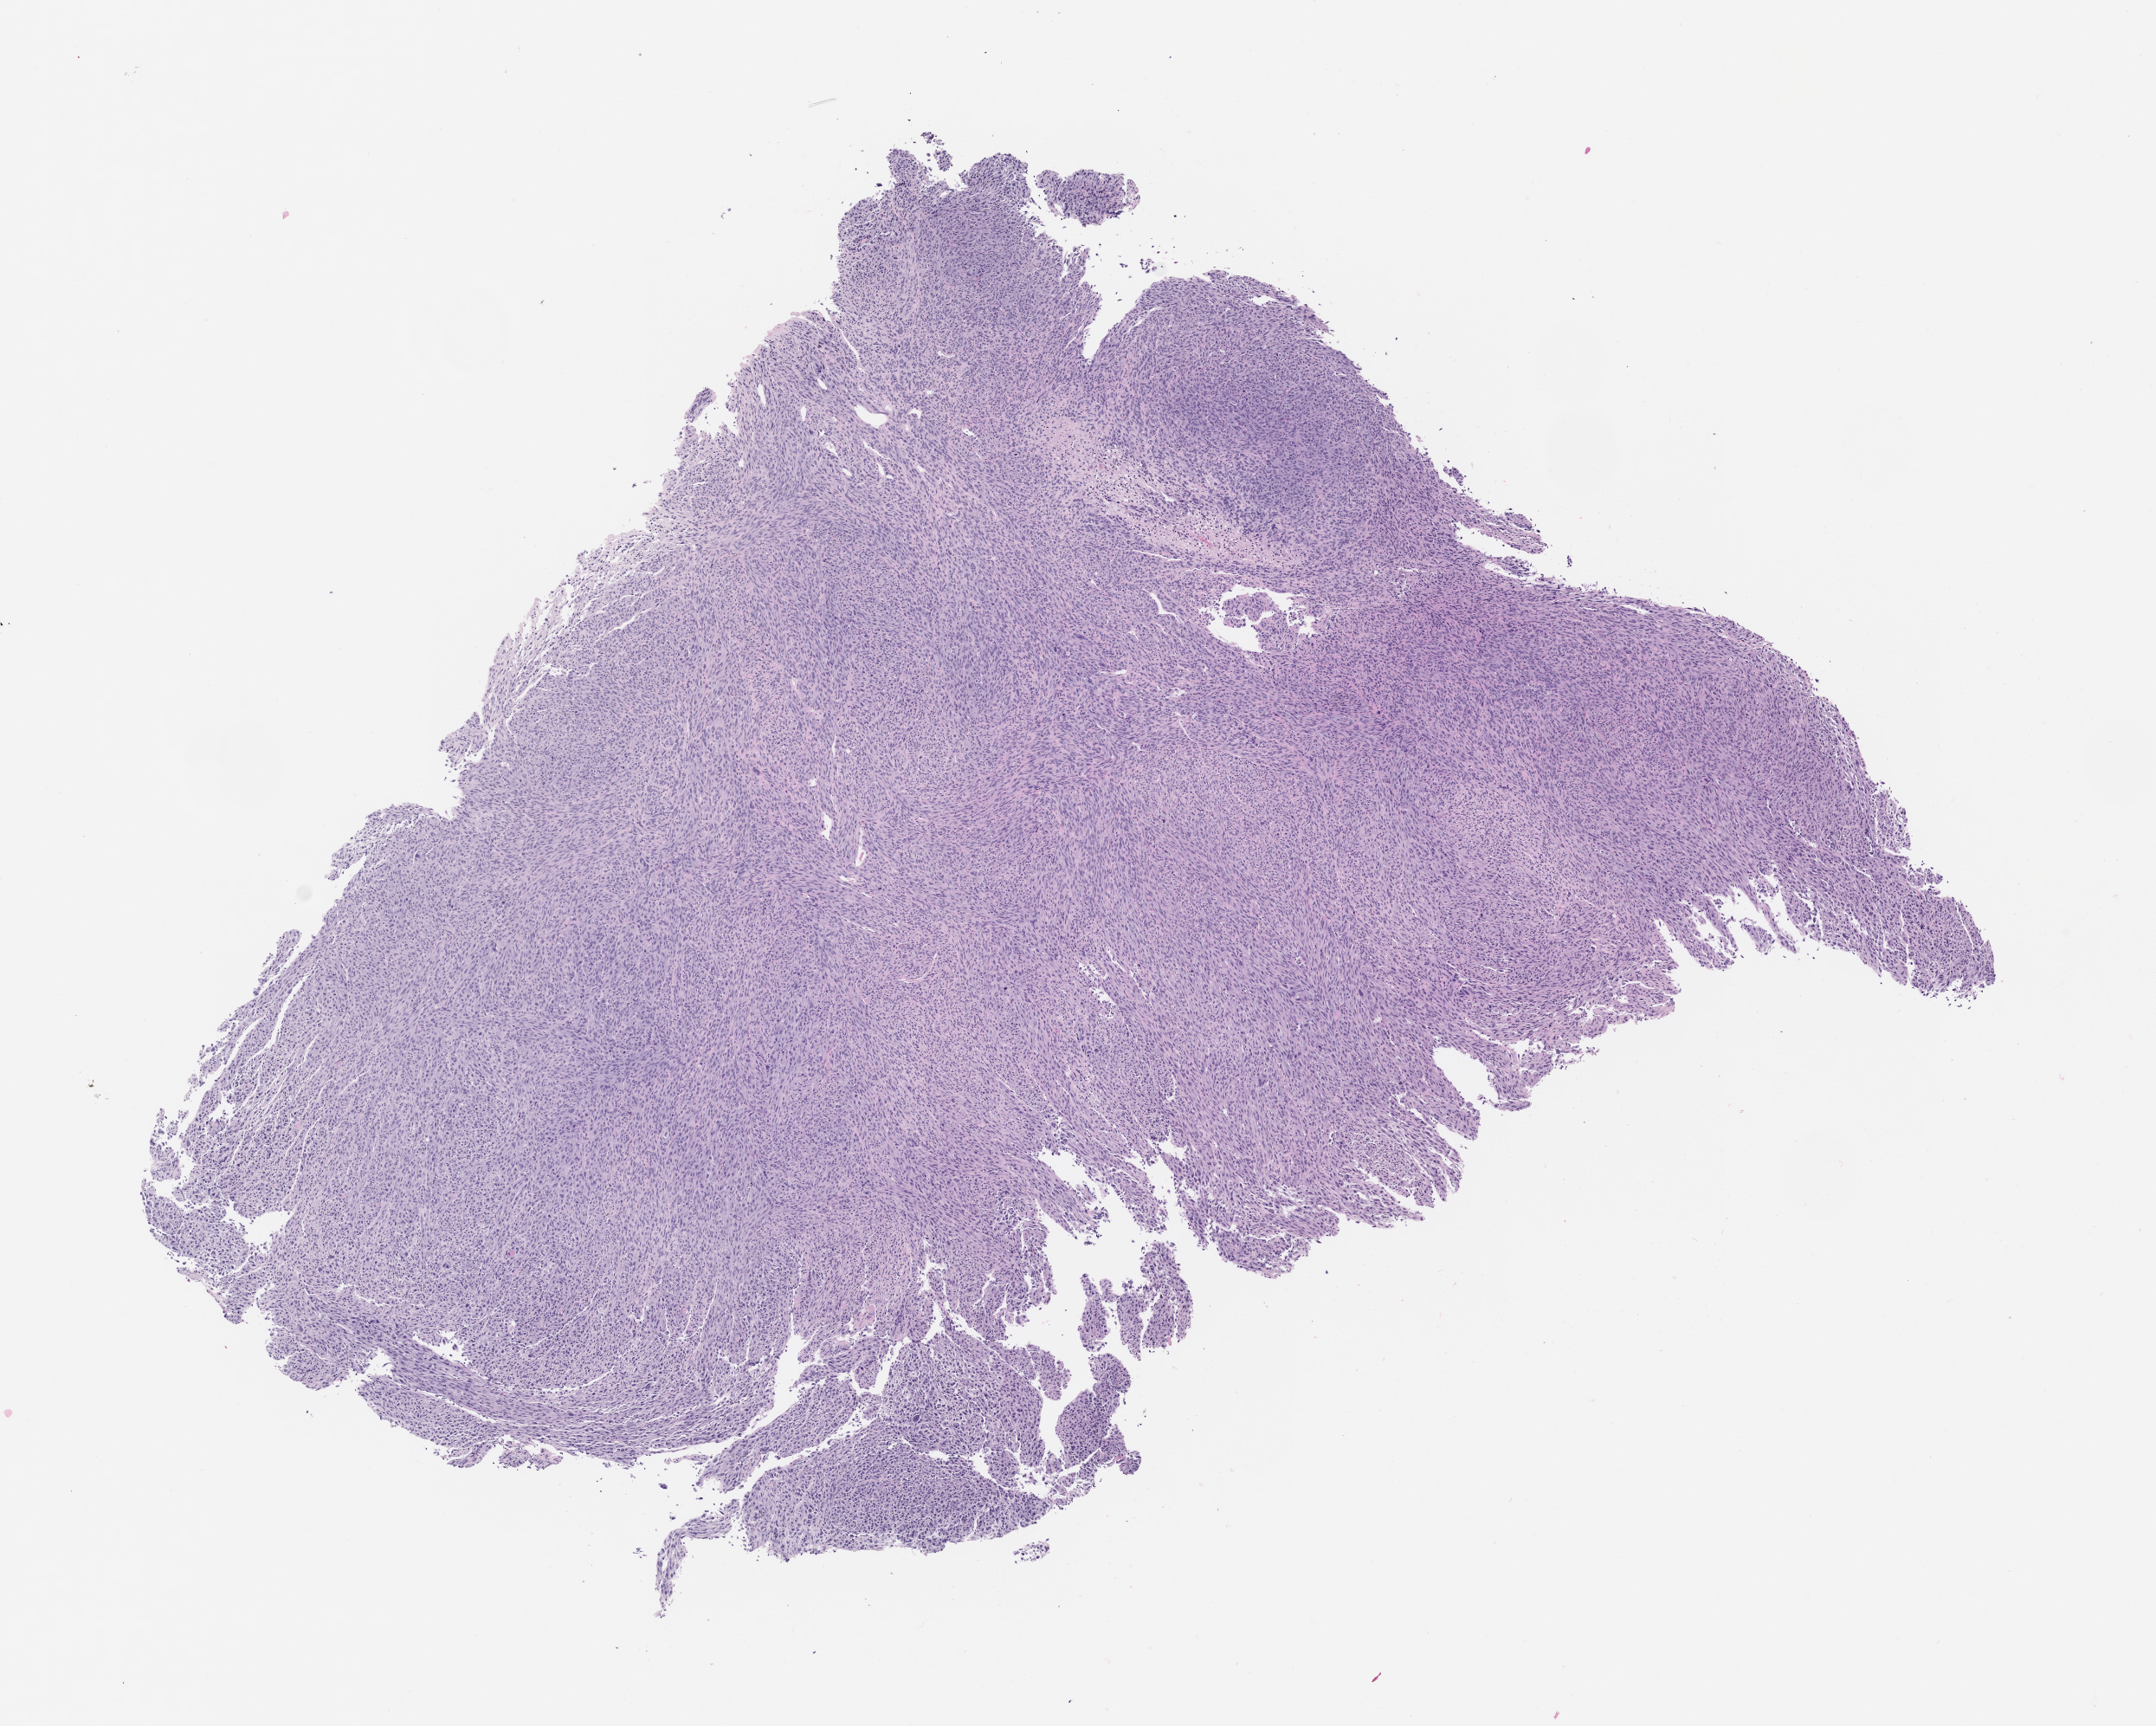
H&E whole-slide image of a patient-derived xenograft (PDX) tumor grown in a mouse, passage 3, a low-resolution overview of the entire scanned area, about 10.0 x 8.0 mm. FFPE section. Originating tumor site category: bone.
Originating patient diagnosis: Osteosarcoma.